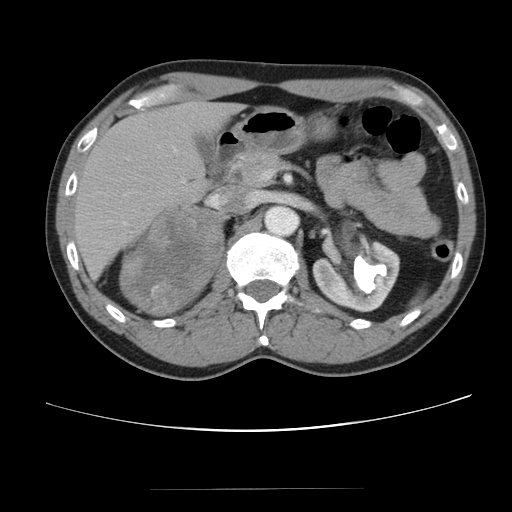
Contrast-enhanced abdominal CT, one axial slice. Intravenous contrast given. Soft-tissue window (W 400 / L 40 HU). 5 mm slice thickness. 512 × 512 image matrix. Patient: male, 61 years. Case-level facts recorded for this patient, not image findings: diagnosis: adrenocortical carcinoma; tumour side: right adrenal.
Outlined on this slice (semi-automatic segmentation, software-assisted and operator-edited):
- mass: bounding box (x1, y1, x2, y2) in pixels: (121, 206, 222, 314)